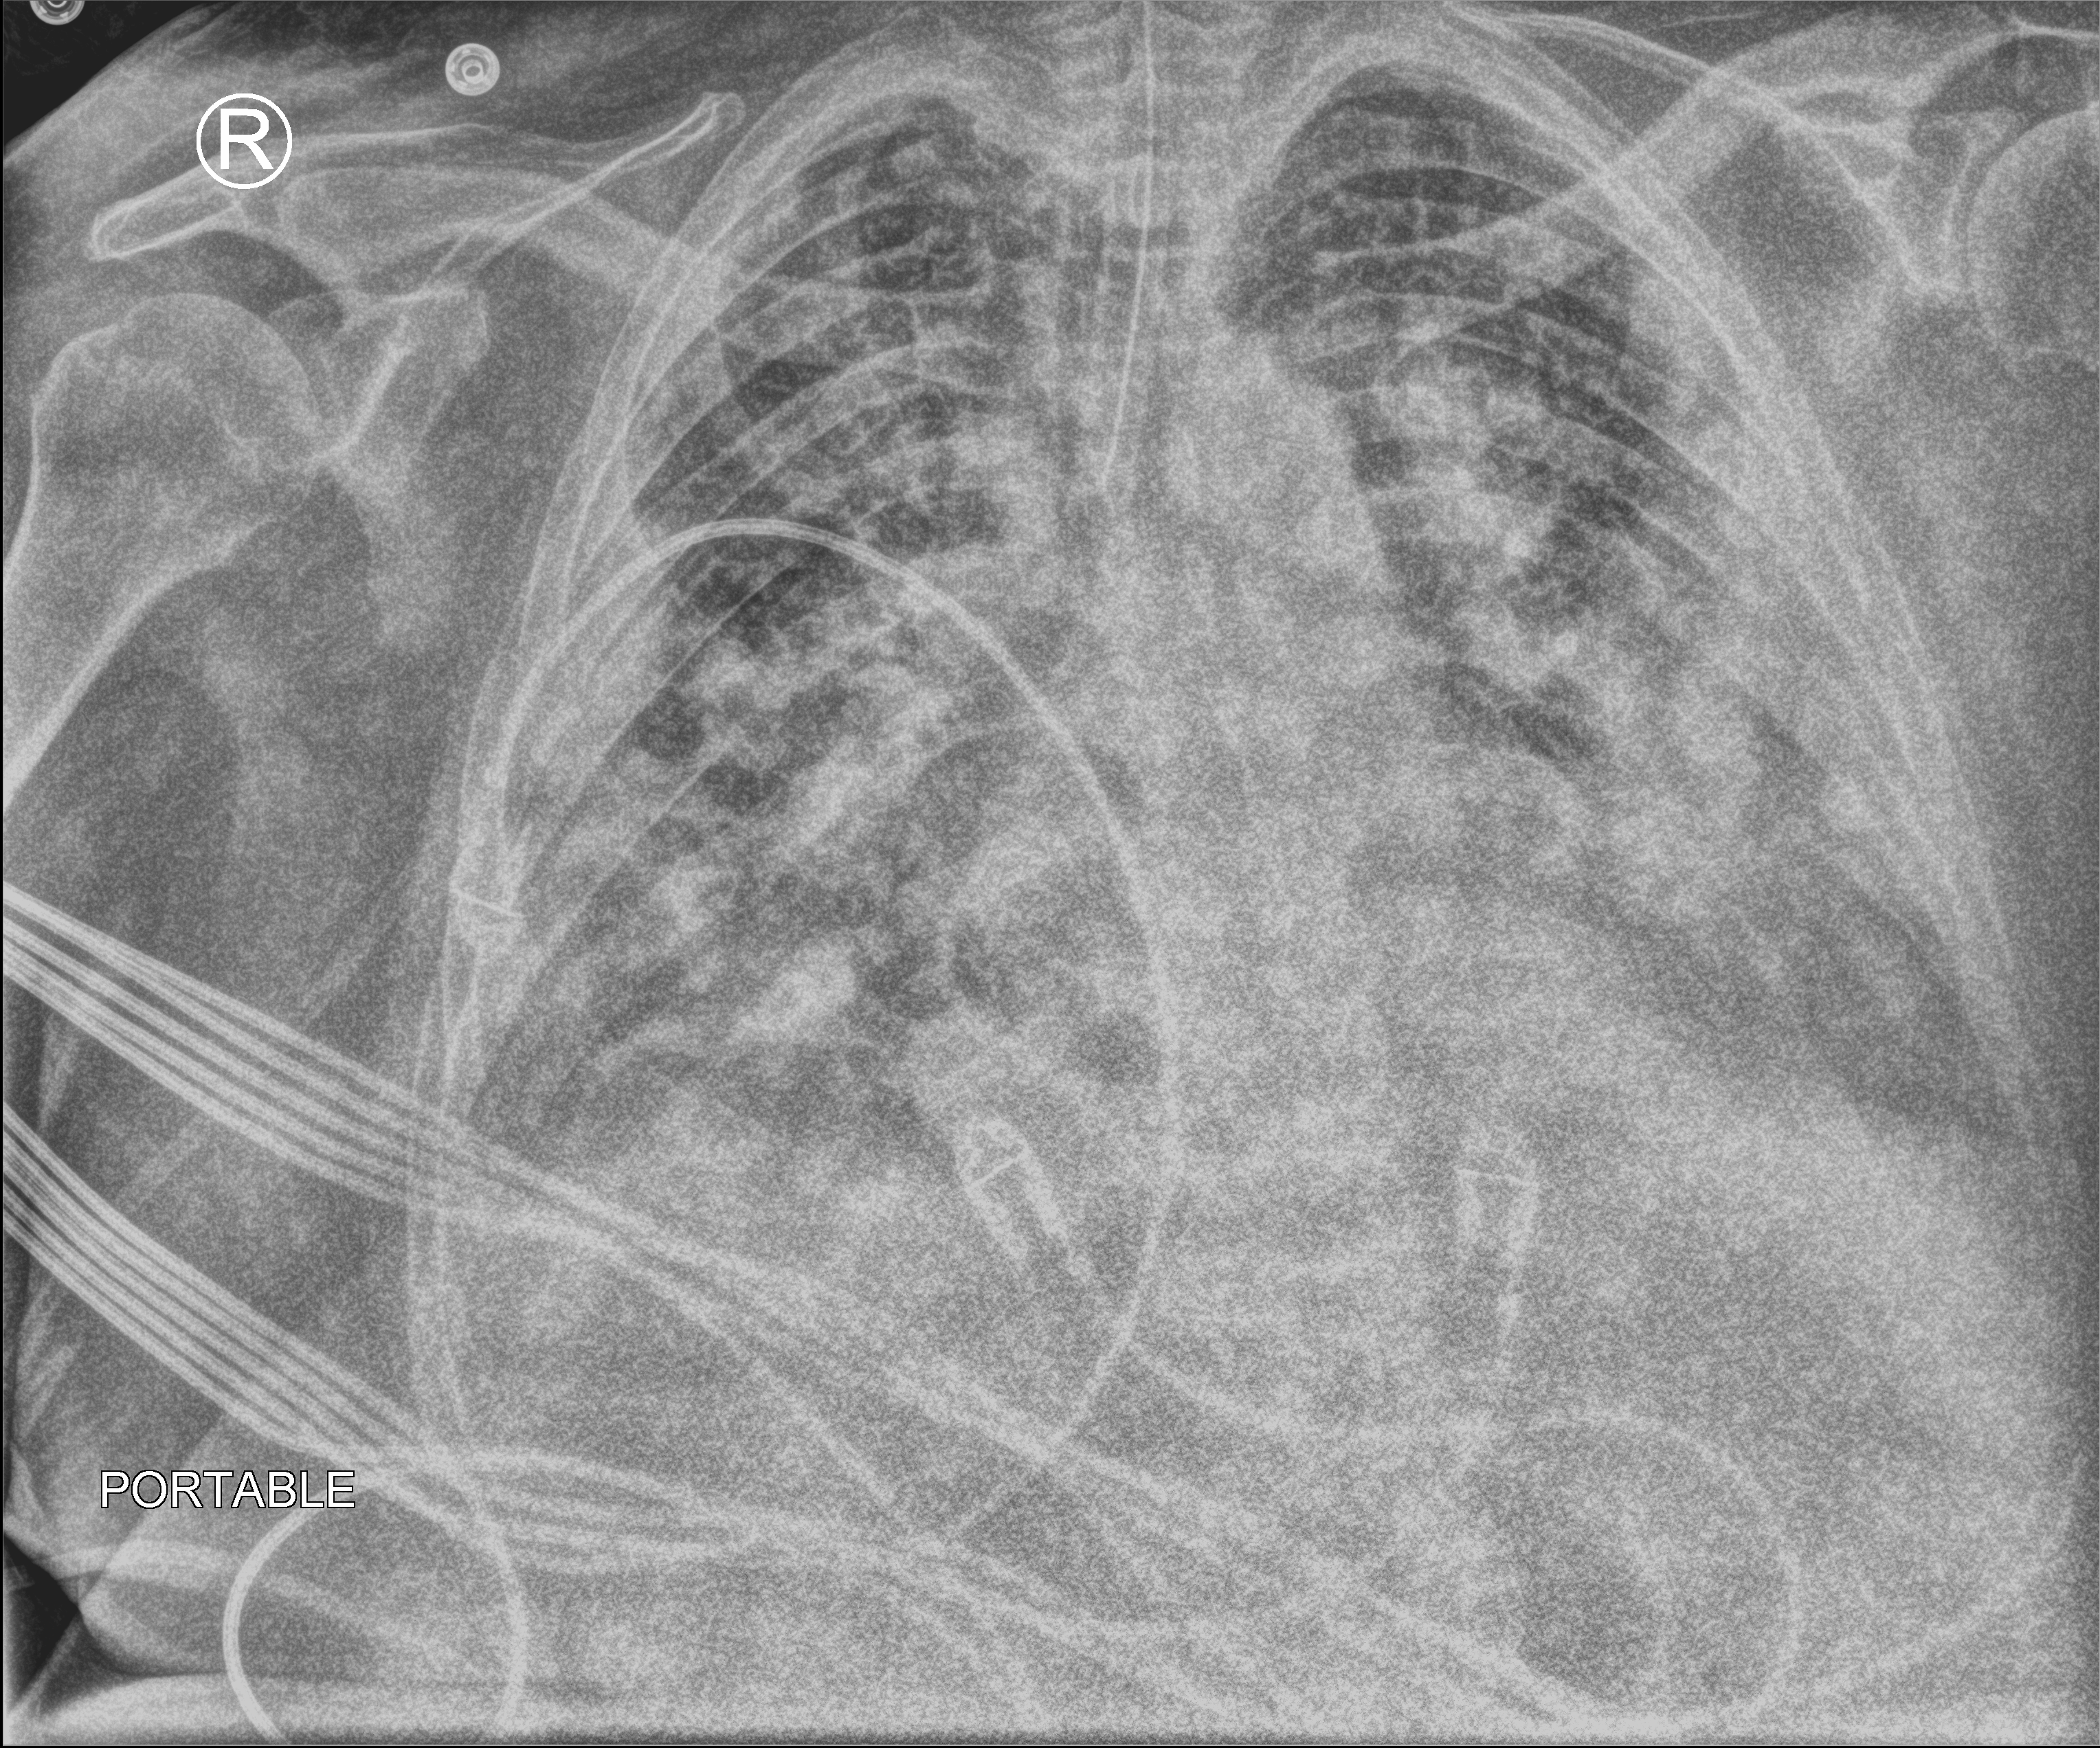
Bedside chest radiograph (computed radiography); anteroposterior (AP) projection. Male patient hospitalised with COVID-19, age 60–74 years.
From the hospital-stay record, not from the radiograph (when in the stay this image was taken is not recorded):
- admitted to intensive care during this hospital stay: yes
- mechanically ventilated during this hospital stay: yes
- length of hospital stay: 7 days